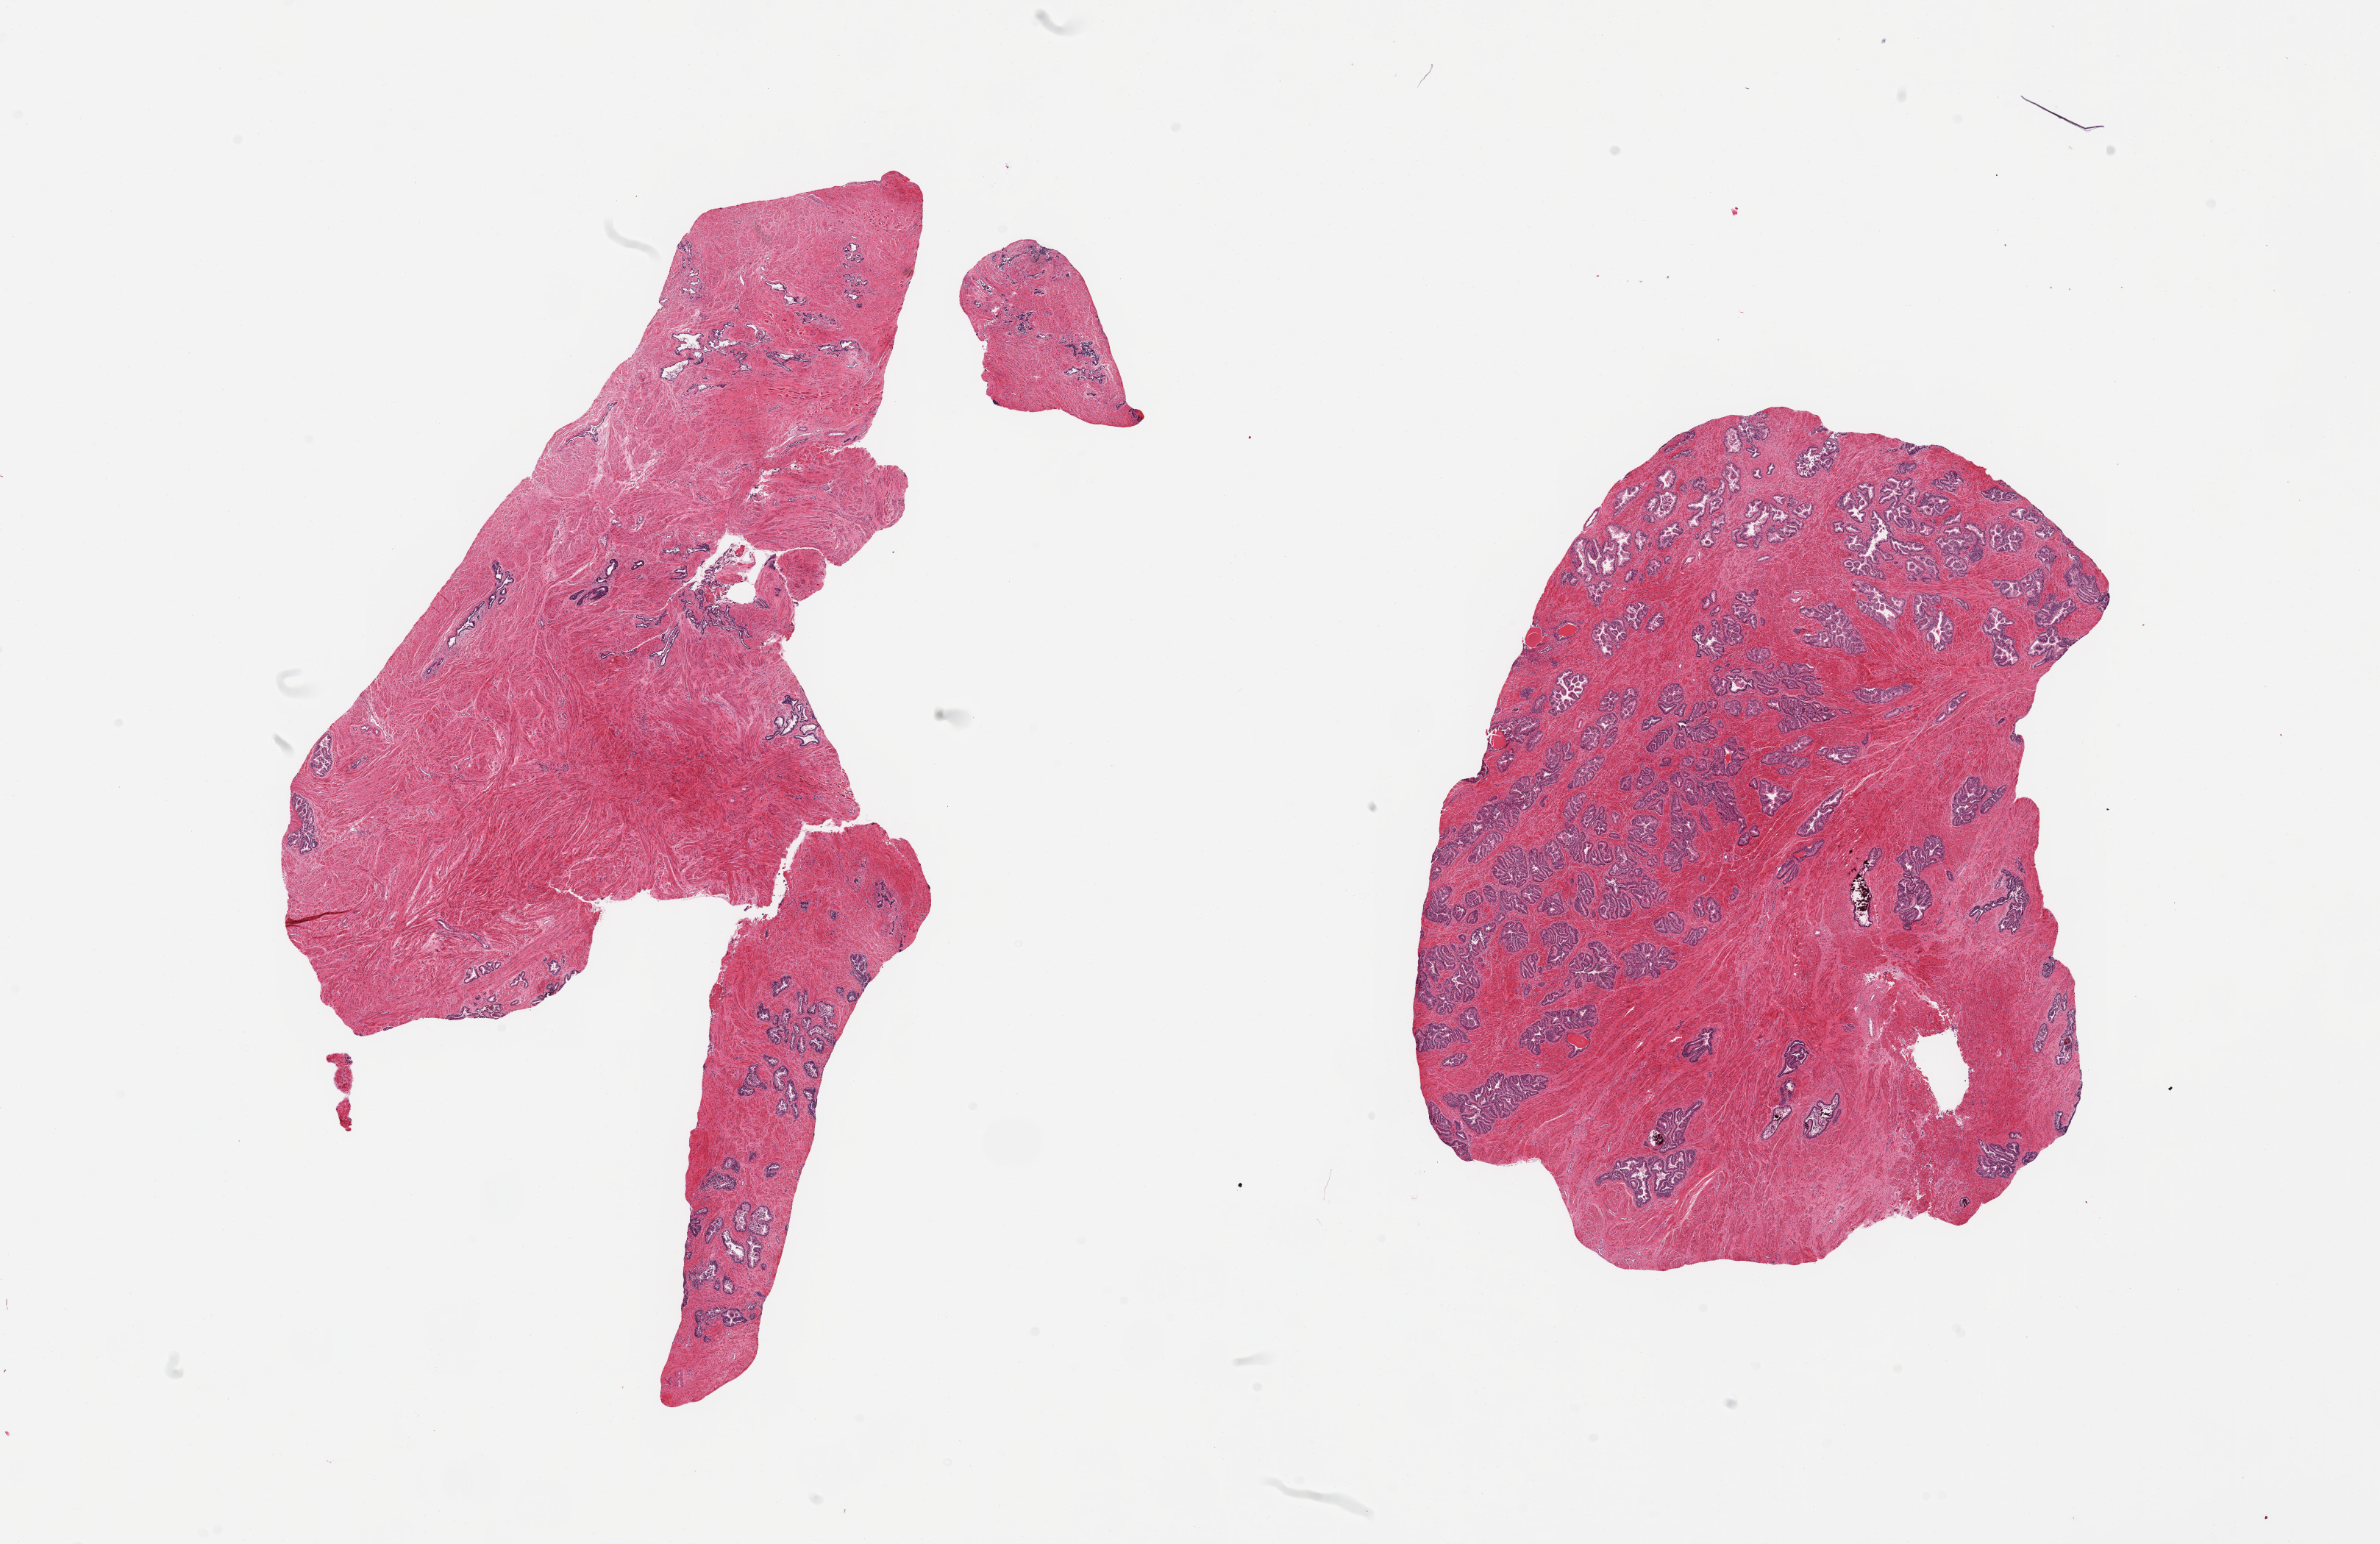
Digitized H&E-stained section, low-resolution overview of the scanned area, about 25.6 x 16.6 mm; PAXgene-fixed paraffin-embedded (PFPE) section; target tissue: prostate; tissue donor sample. Donor: male.
- pathologist's review note for this sample: 2 pieces; one piece has good admixture of stroma and glands, second is predominantly stroma